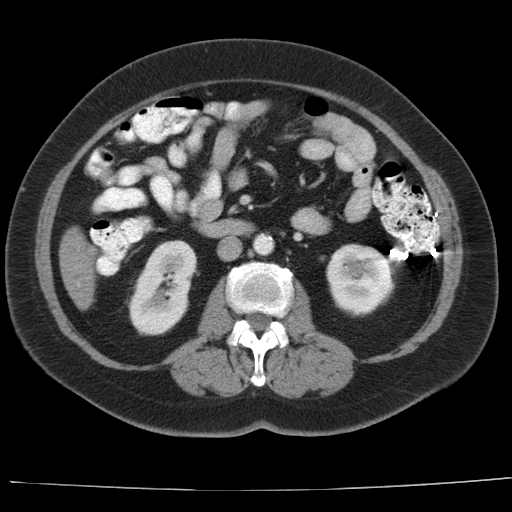
Contrast-enhanced abdominal CT, one axial slice; slice 4 of 44 in the series (ordered by position); 140 kVp; intravenous contrast given; soft-tissue window (W 400 / L 40 HU); 5 mm slice thickness; 512 × 512 image matrix, field of view 373 × 373 mm. Female patient. From the clinical record (not read from this slice): diagnosis: colorectal cancer liver metastases, imaged before liver resection; multiple liver metastases: yes.
Outlined on this slice (manually delineated by an expert):
- liver: bounding box [x1, y1, x2, y2] px = [60, 230, 96, 308]